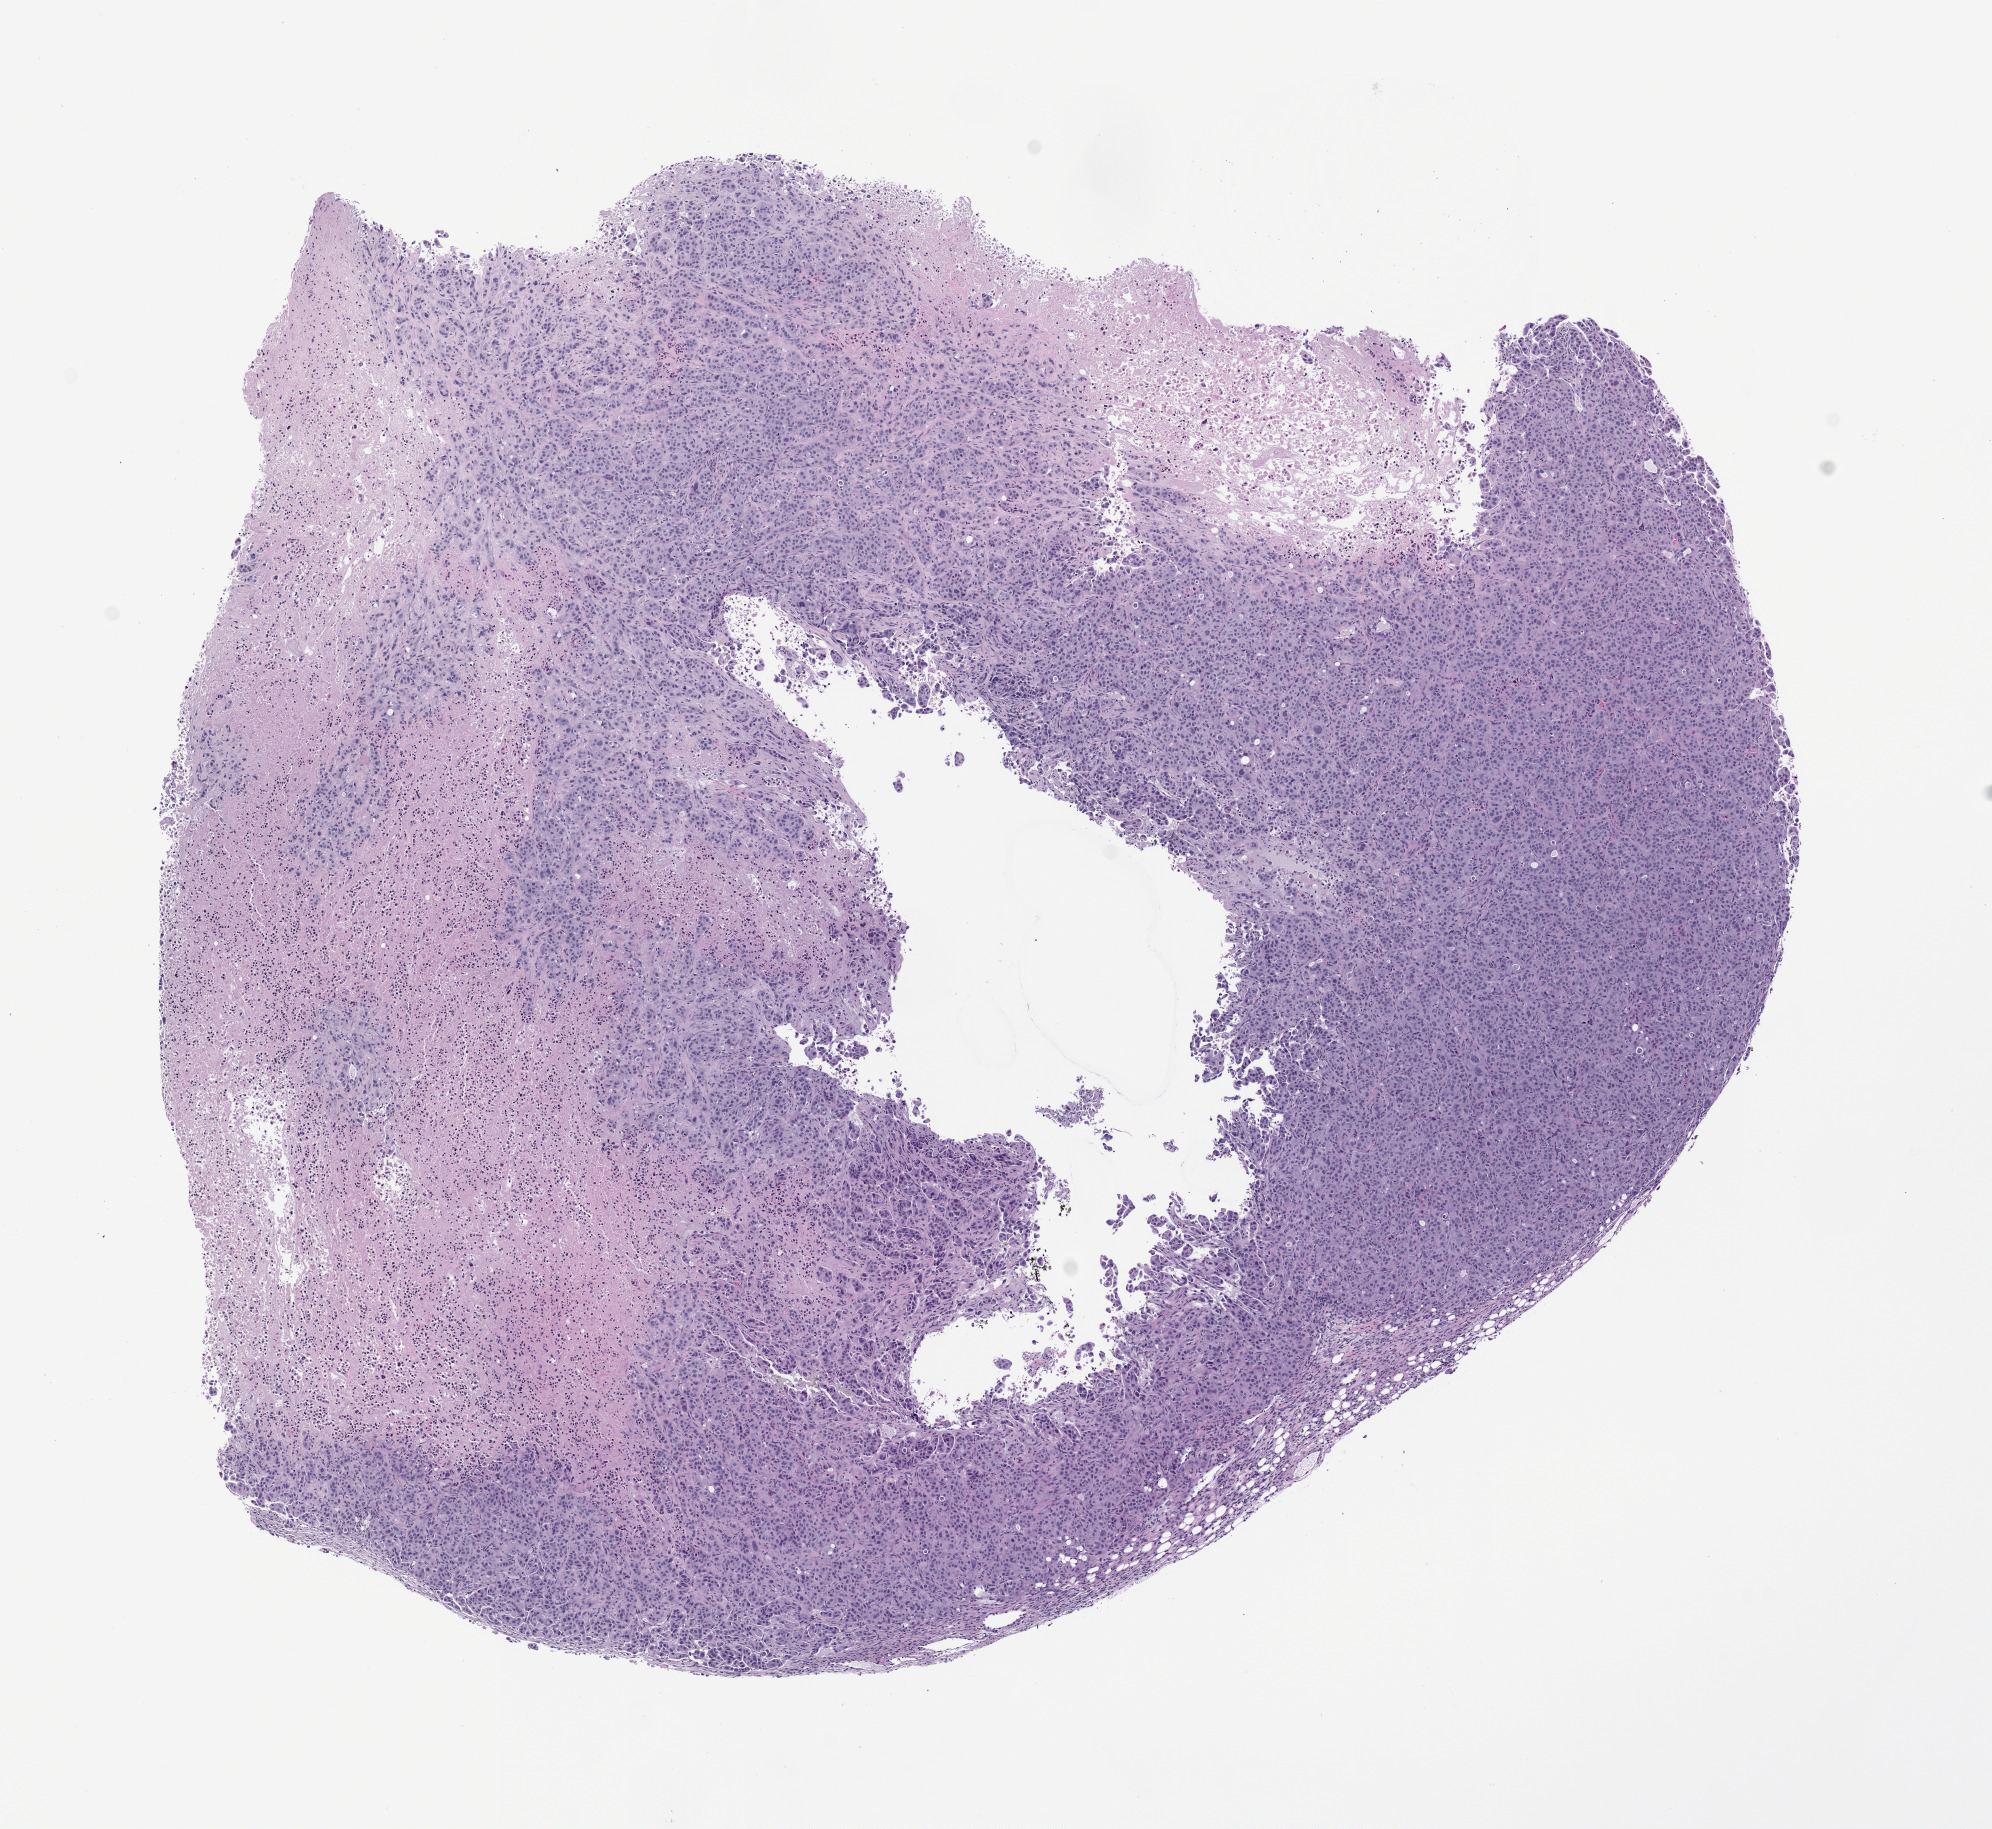
H&E whole-slide image of a patient-derived xenograft (PDX) tumor grown in a mouse — whole scanned area (about 8.0 x 7.4 mm) shown as a low-resolution overview. Formalin-fixed paraffin-embedded section. Tumor site category: lung.
Originating patient diagnosis: Lung Squamous Cell Carcinoma.